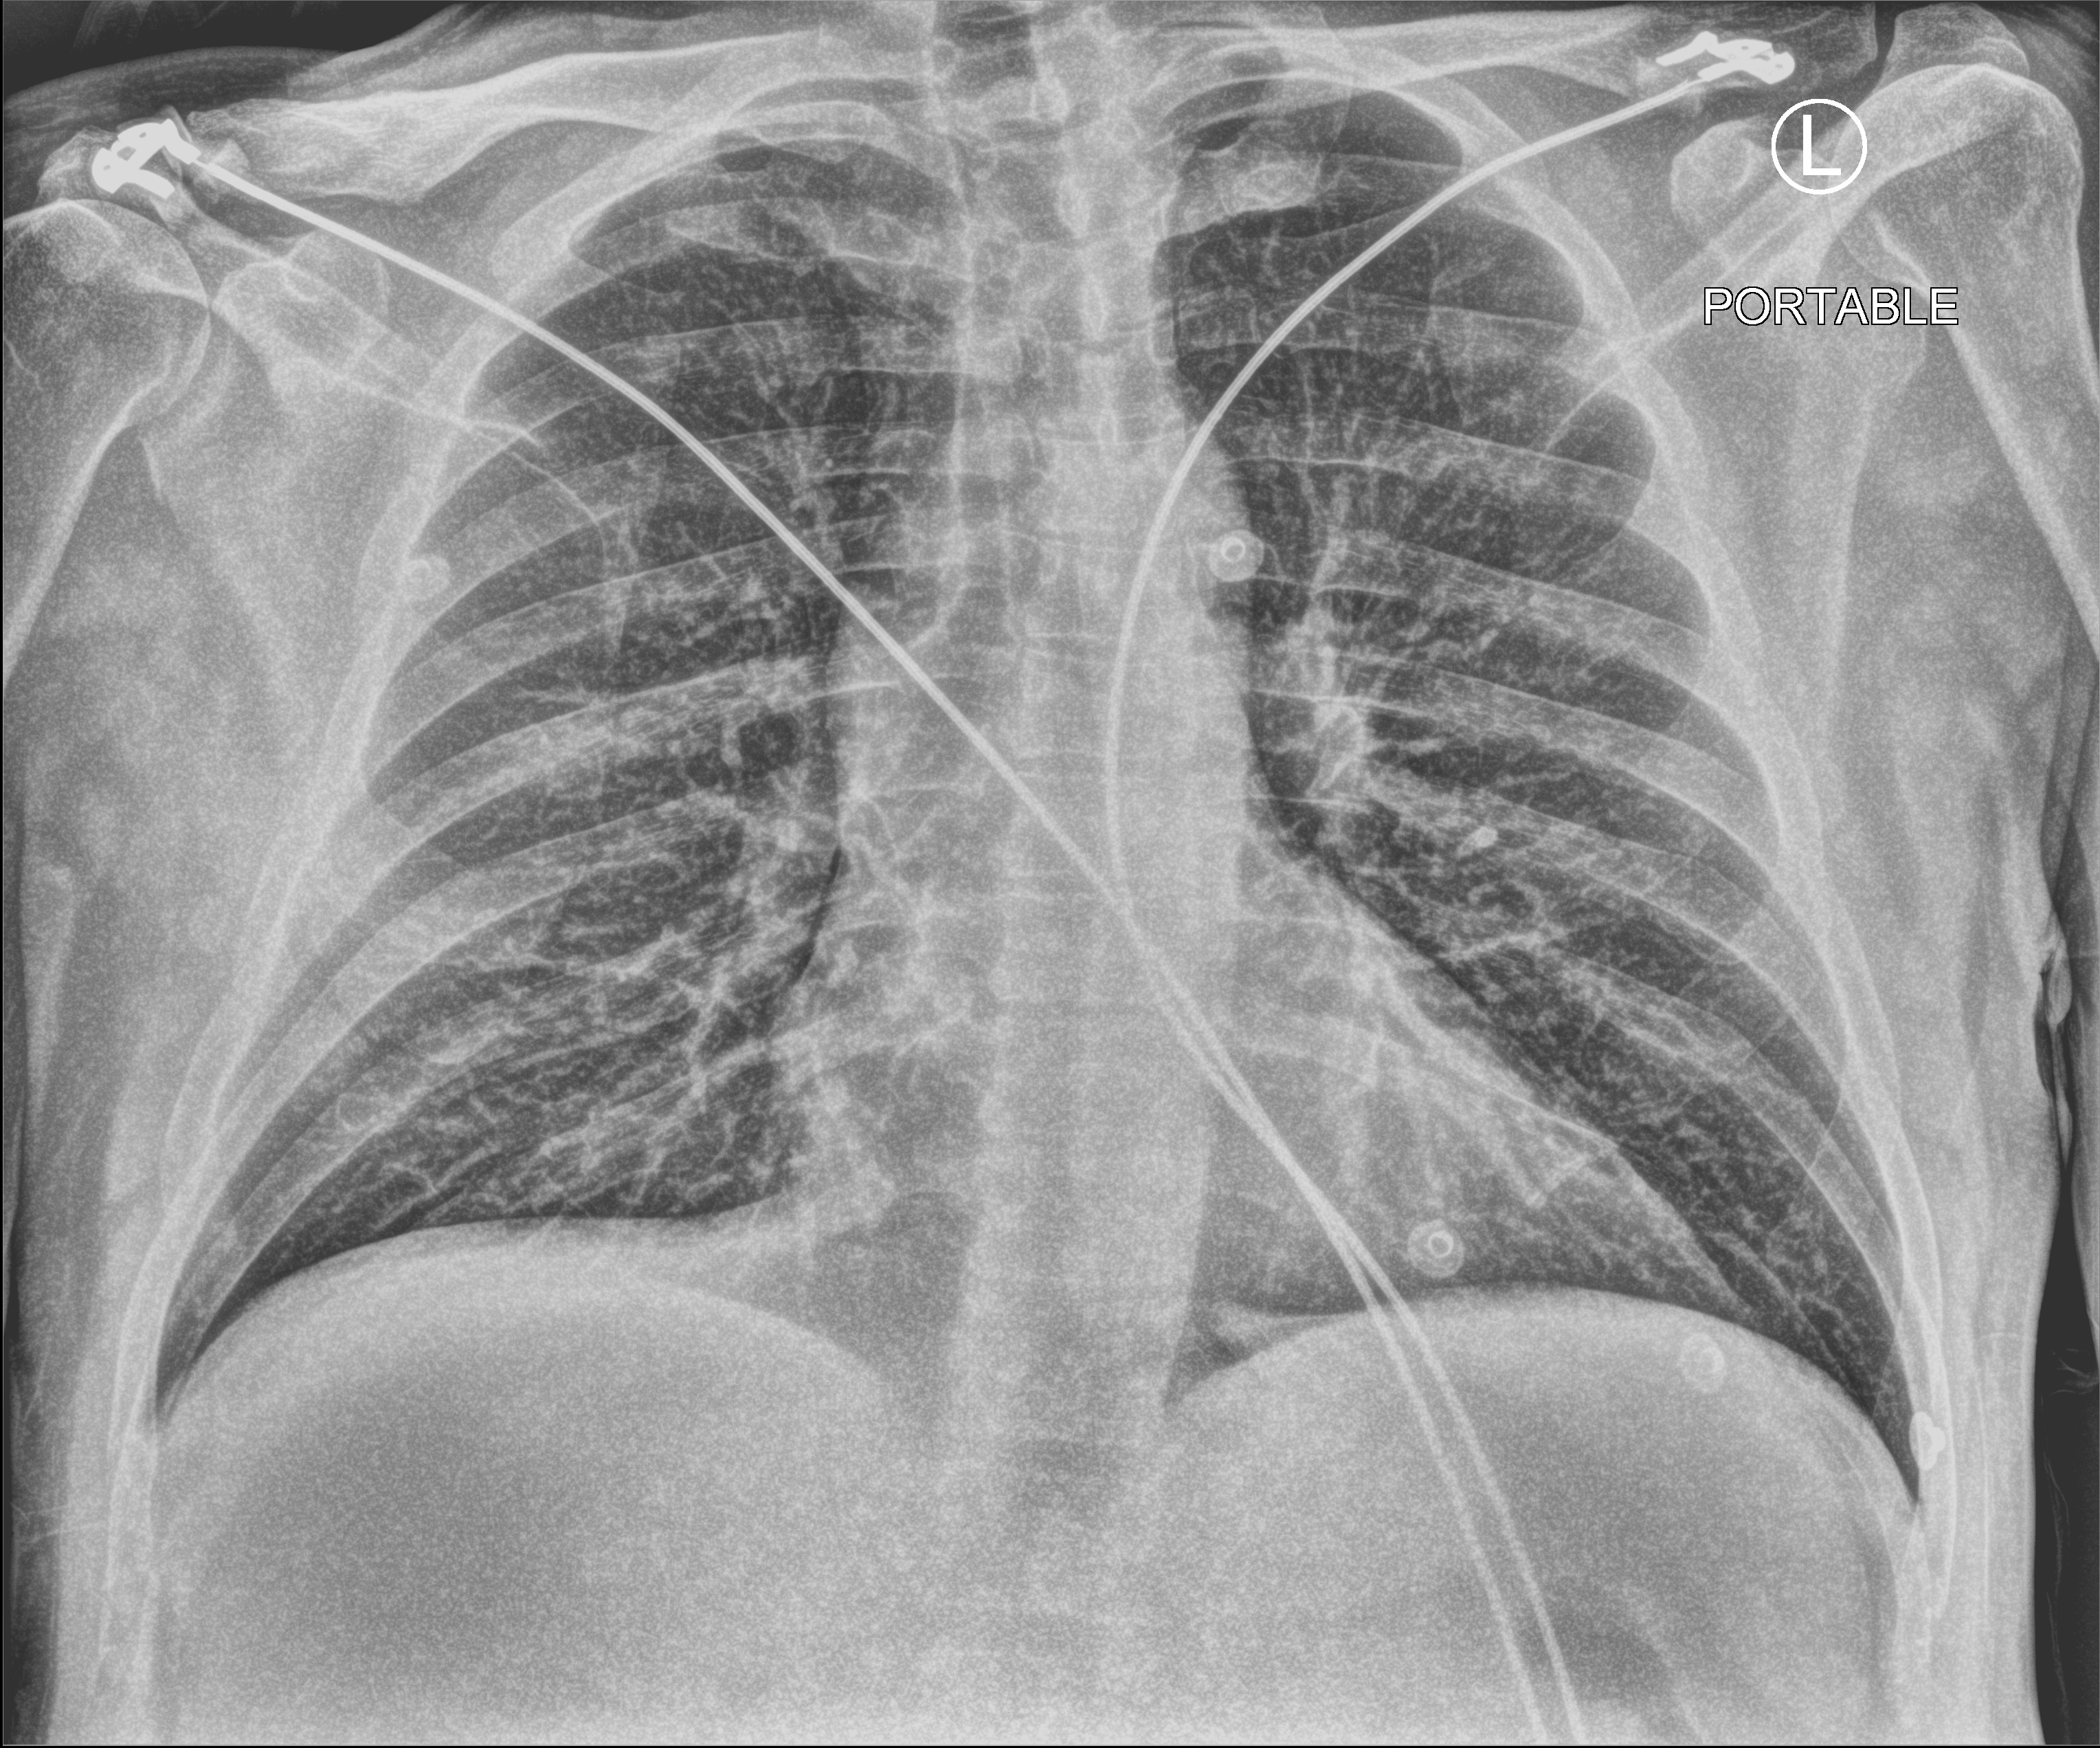
Bedside chest radiograph (computed radiography), anteroposterior (AP) projection. Male patient hospitalised with COVID-19, age 18–59 years.
From the hospital-stay record, not from the radiograph (when in the stay this image was taken is not recorded): length of hospital stay: 2 days.